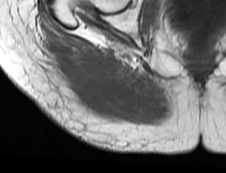
MRI of an extremity soft-tissue mass, one axial slice. Slice 26 of 73 in the series (ordered by position). MR volume resampled by the dataset authors to the PET/CT grid (not the native acquisition matrix). 226 × 173 image matrix. Female patient. From the clinical record (not read from this slice): histological type: spindle cell suggestive of myxofibrosarcoma; grade: intermediate; site of the primary tumour: right buttock.
Structures marked on this image (expert contour drawn on MRI and transferred to this co-registered scan by the dataset authors):
- gross tumour volume (mass): bounding box [x1, y1, x2, y2] px = [45, 42, 126, 112]